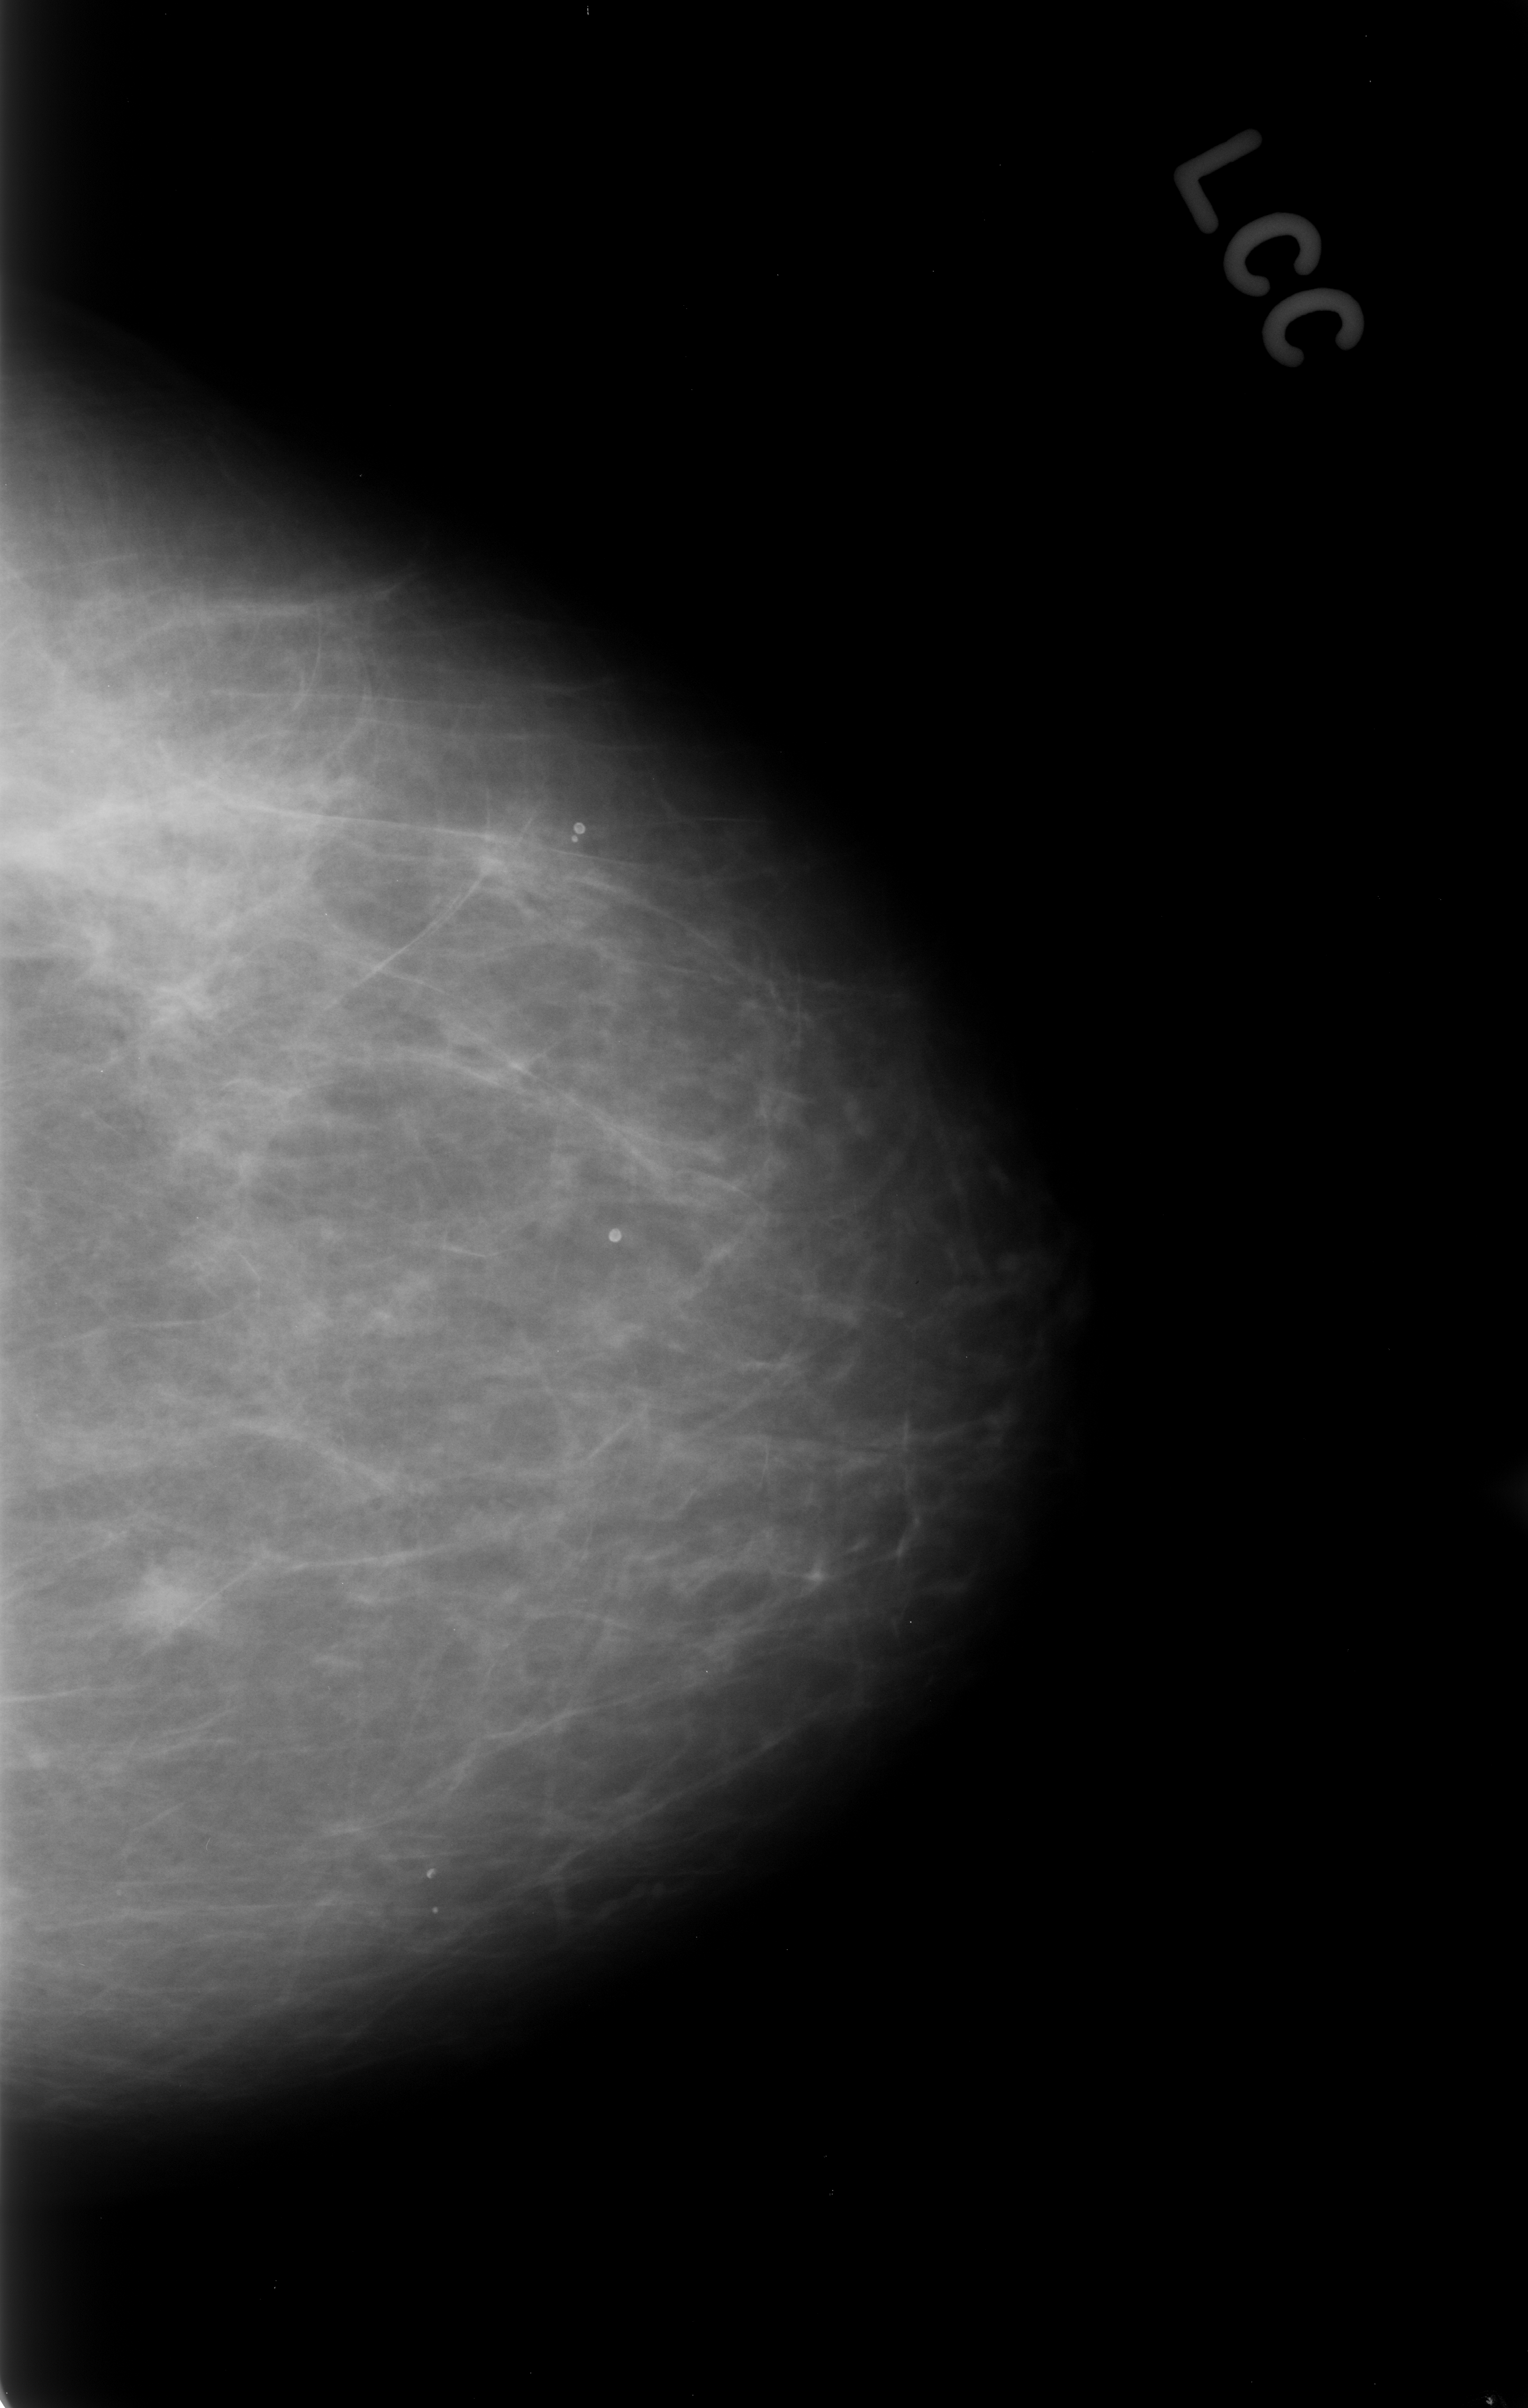
Digitized screen-film mammogram, left breast, craniocaudal (CC) view.
Marked abnormality: mass, shape irregular, margins microlobulated; BI-RADS assessment category 3; benign without callback (not worked up further).